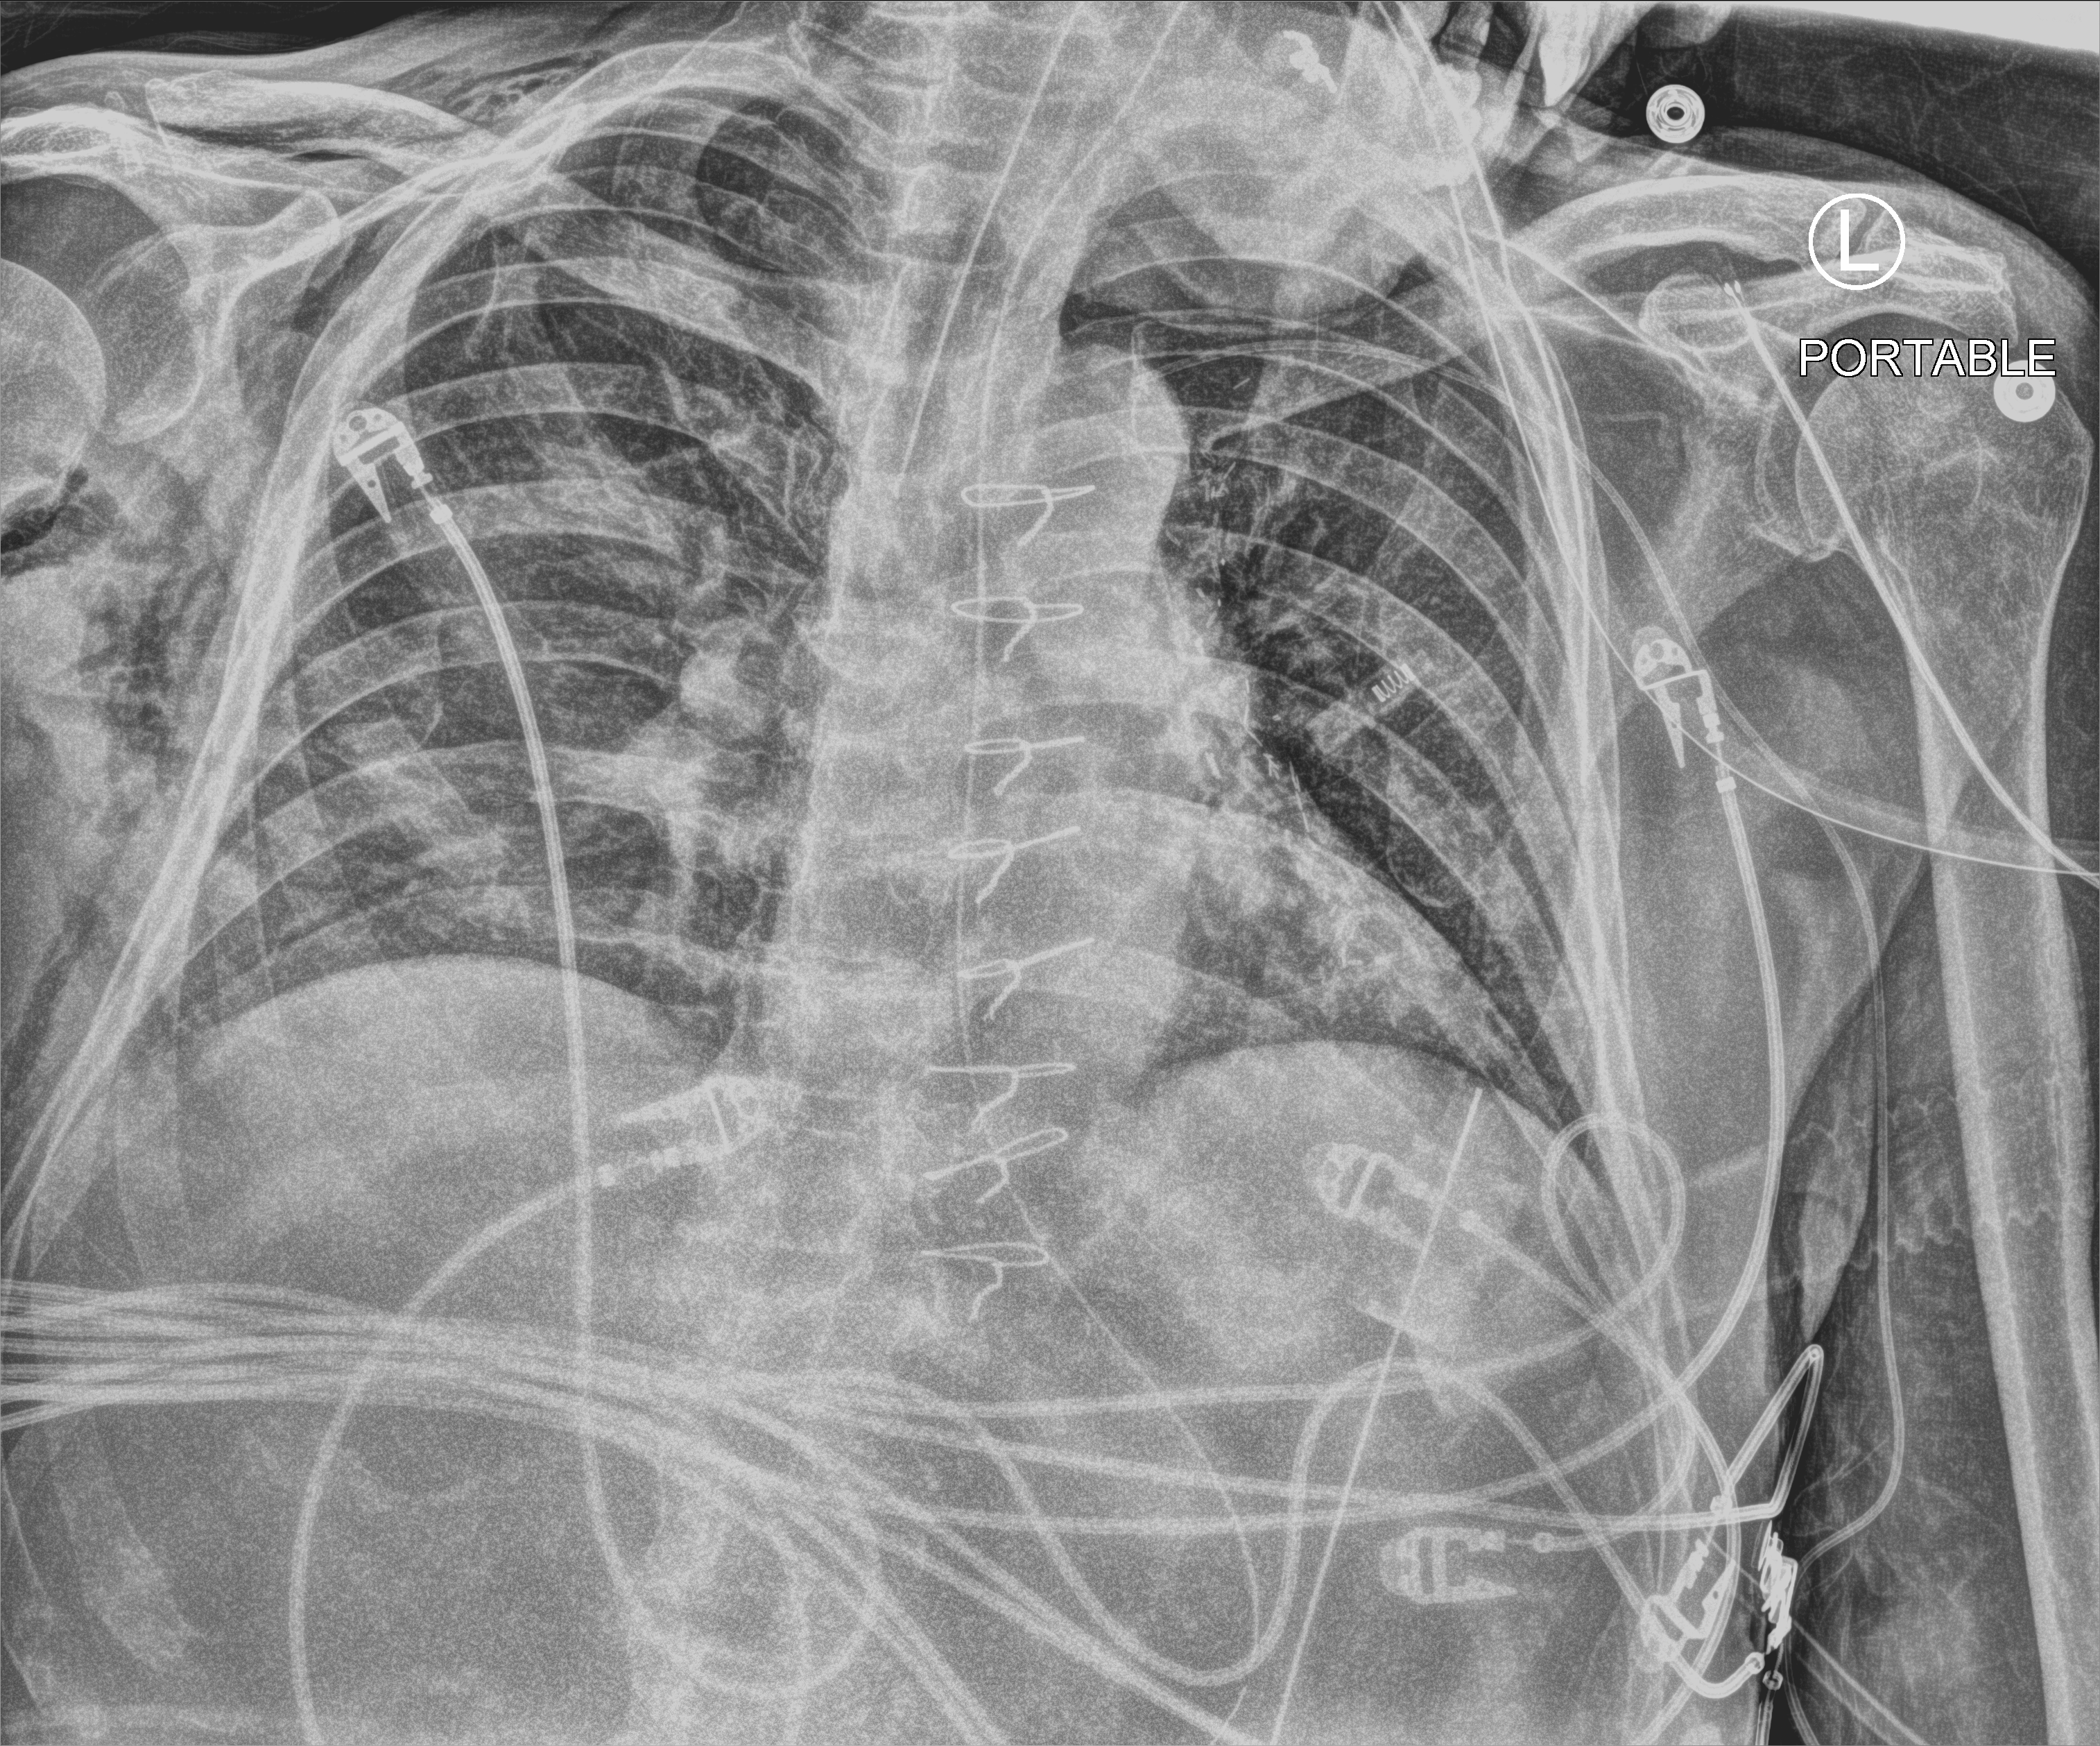
Bedside chest radiograph (computed radiography), anteroposterior (AP) projection. Patient hospitalised with COVID-19; male, aged 60–74 years.
Hospital-stay facts (about this admission, not read from this image; timing relative to this image not recorded):
- admitted to intensive care during this hospital stay: yes
- length of hospital stay: 22 days